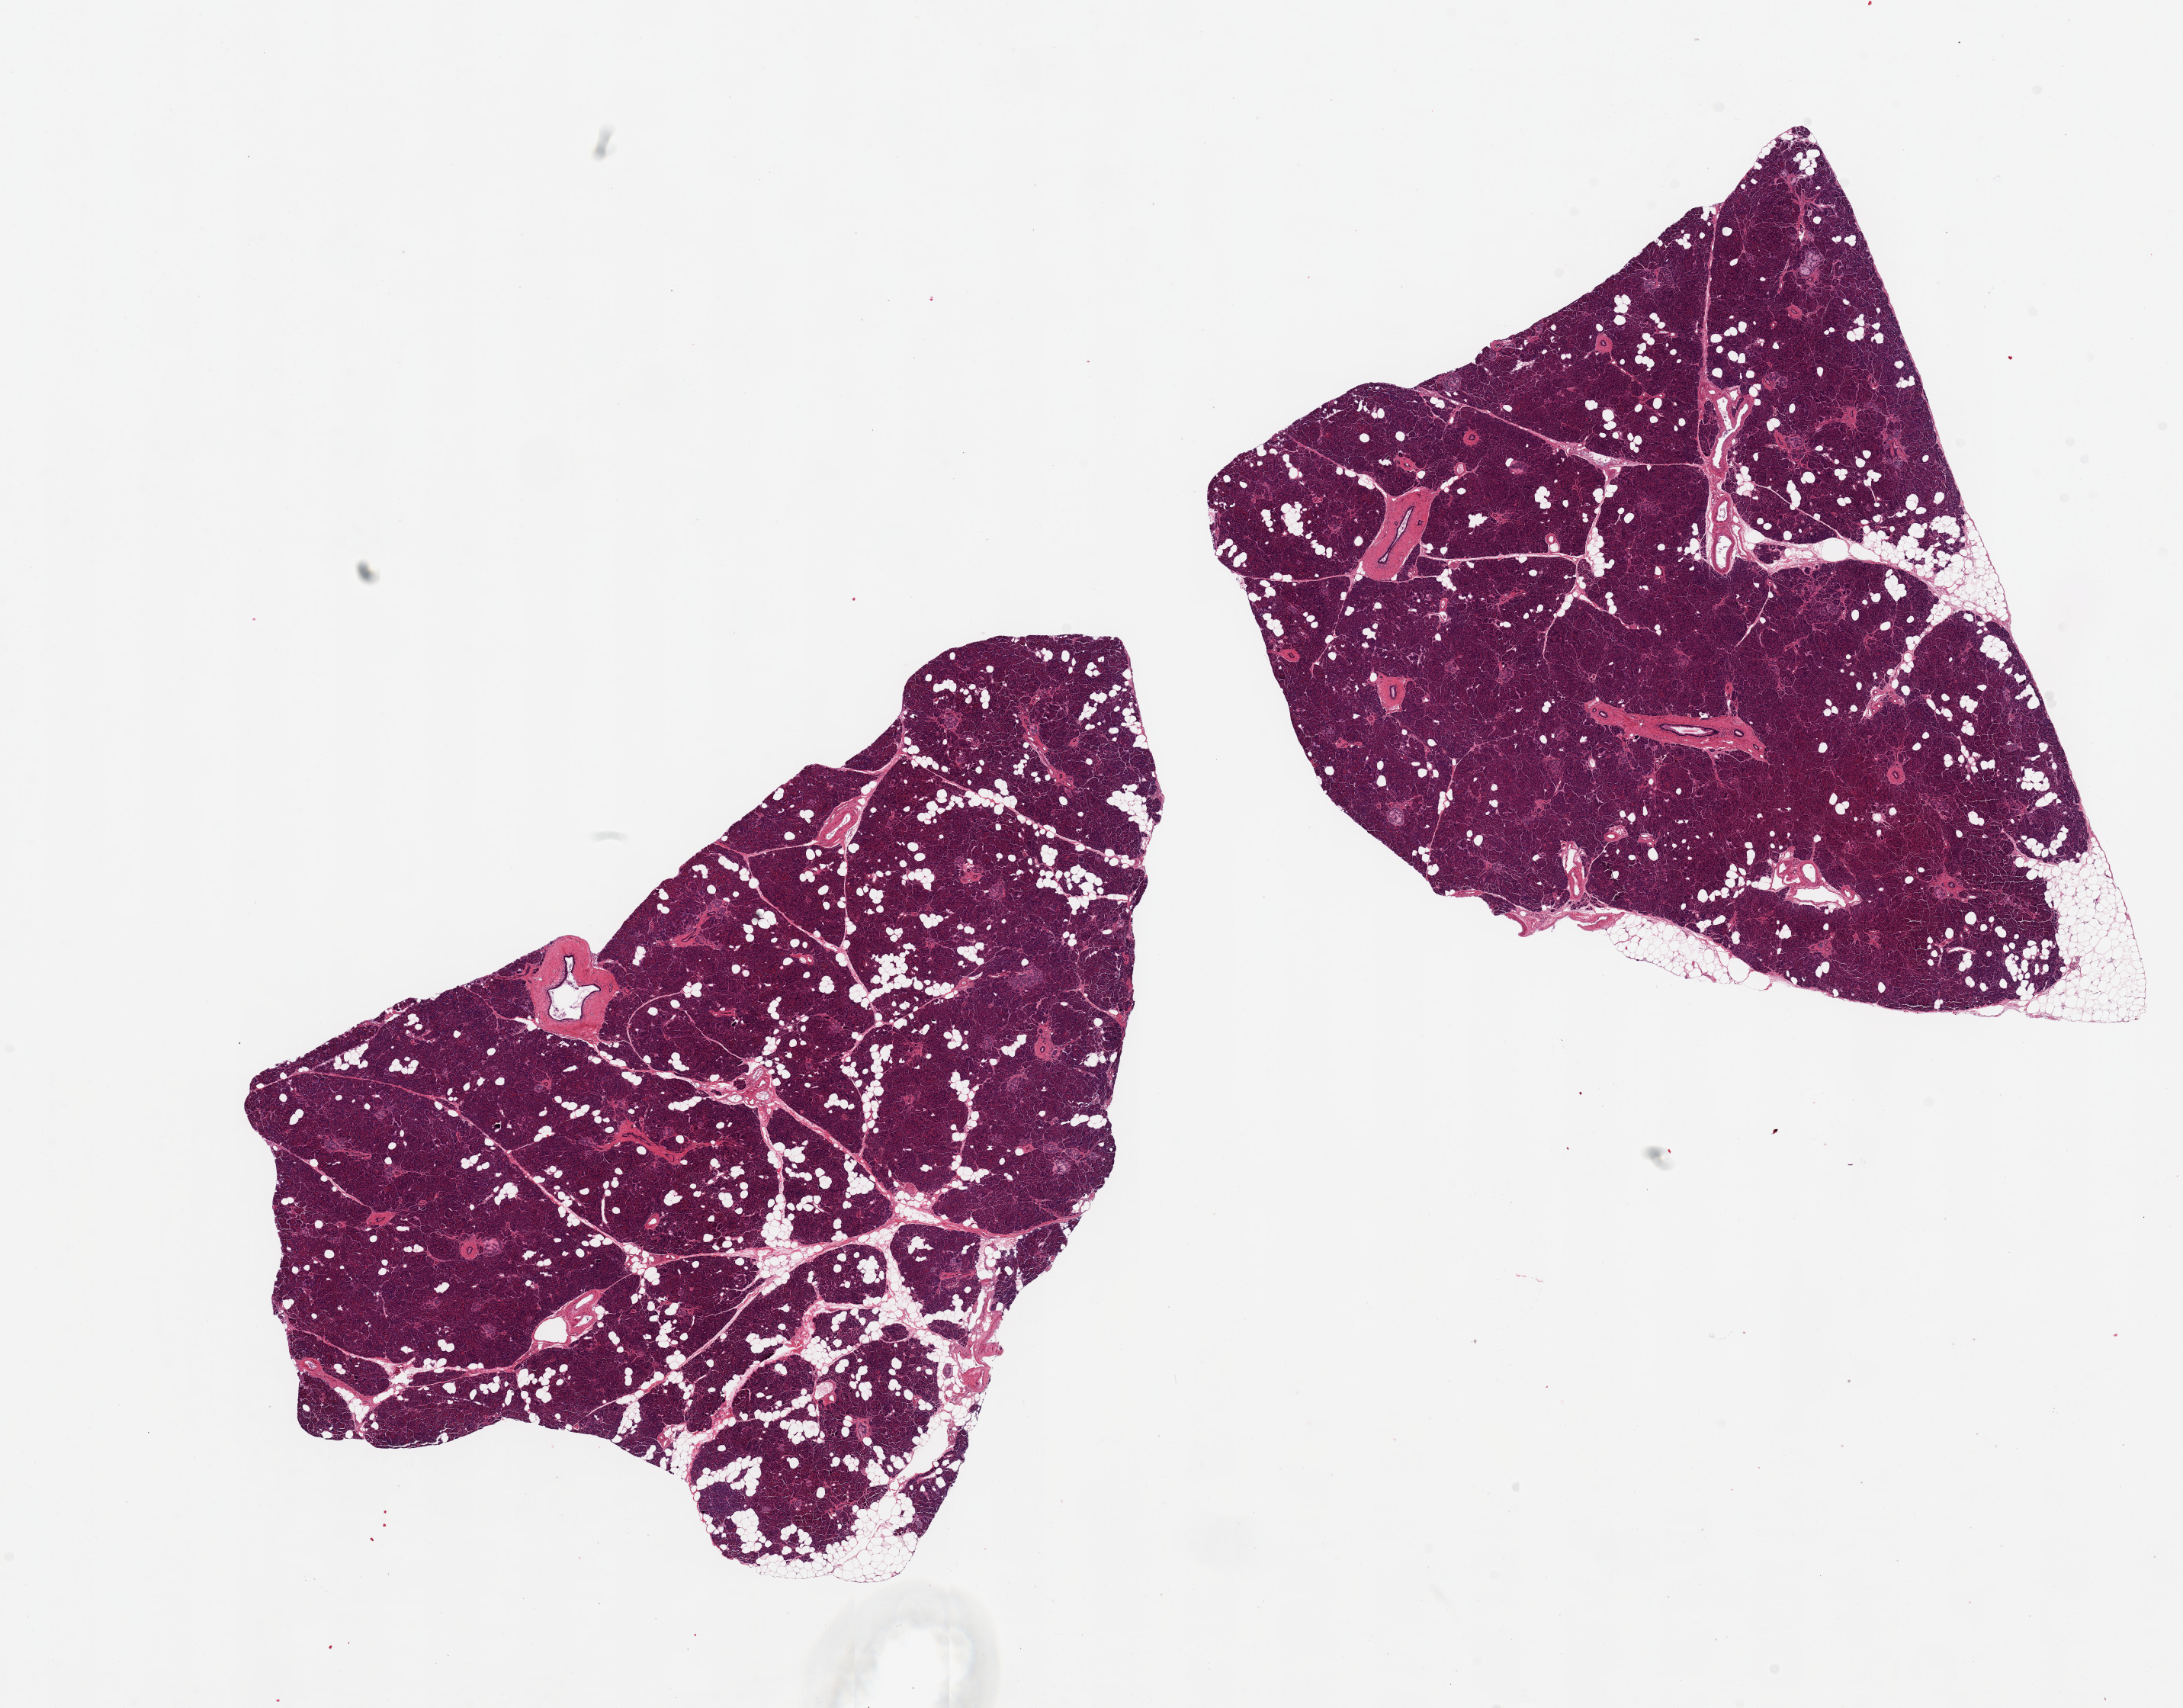
Whole-slide image, haematoxylin and eosin stain, a low-resolution overview of the entire scanned area, about 22.6 x 17.7 mm (slide scanned at 20x); PAXgene-fixed paraffin-embedded (PFPE) section; section of pancreas (target tissue); tissue donor sample. Donor sex: male.
Reviewer comment on this tissue sample: 2 aliquots ~10x6mm, remarkably well-preserved.